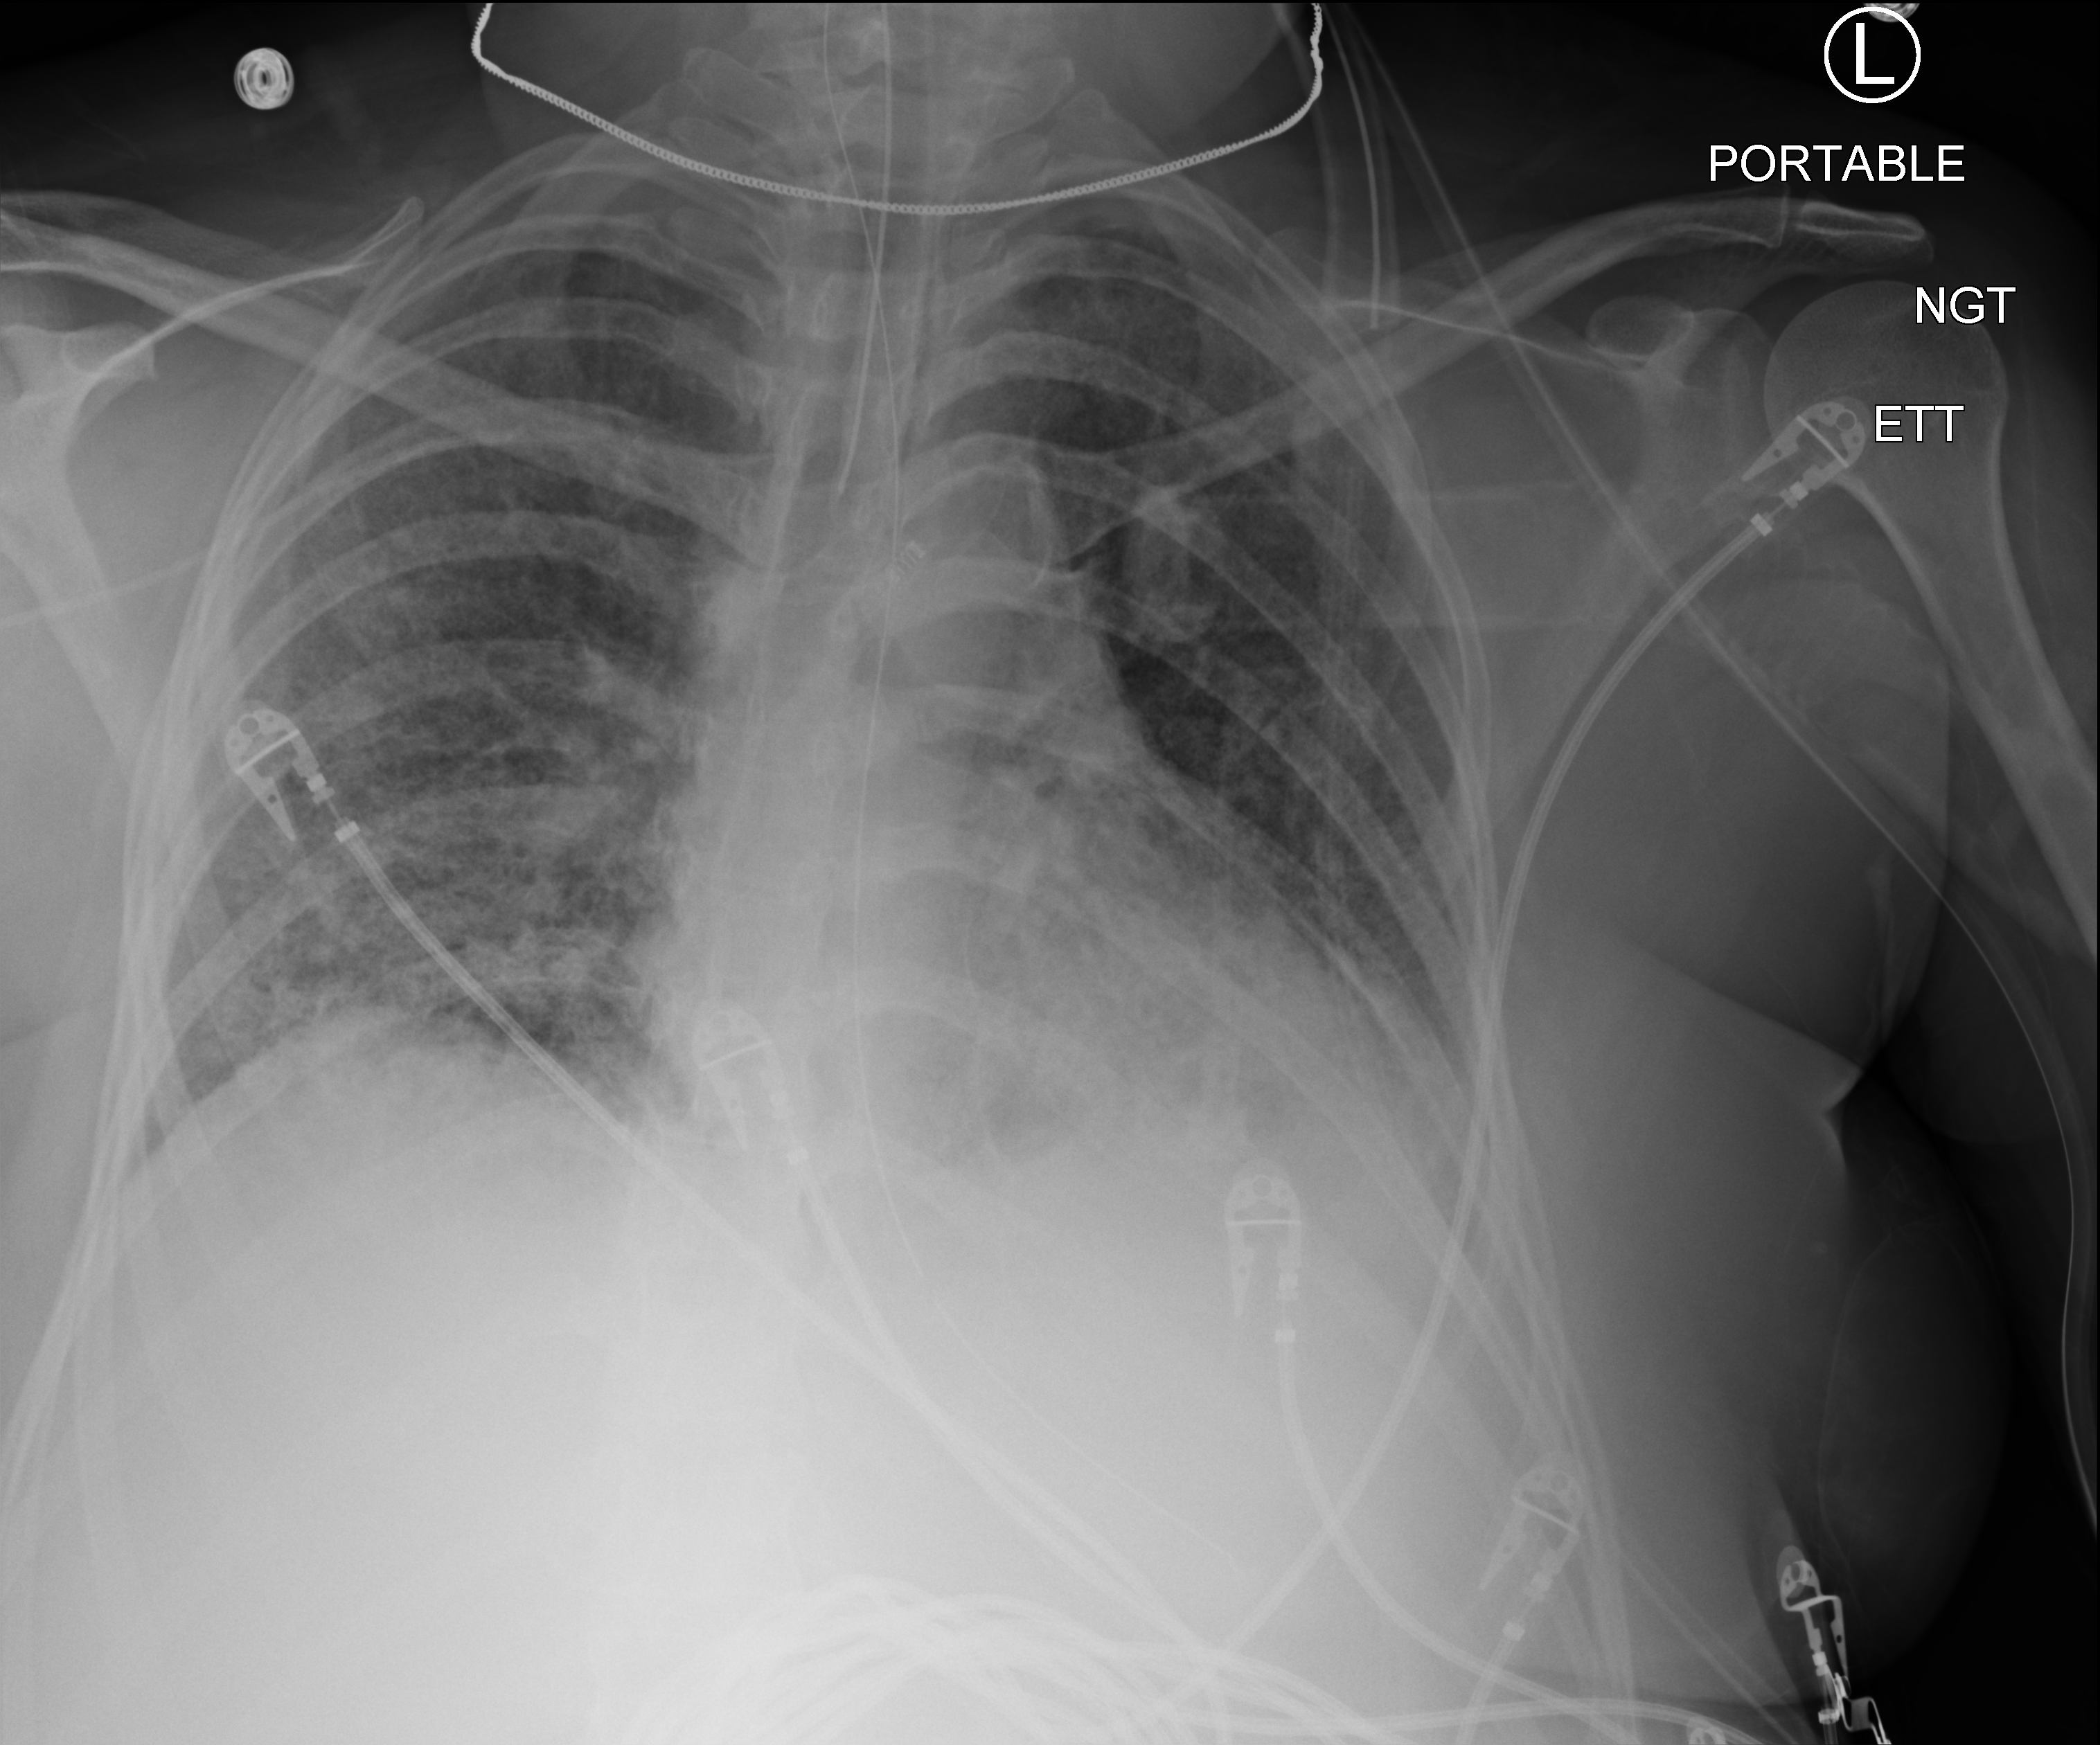
Bedside chest radiograph (computed radiography). Female patient hospitalised with COVID-19, age 18–59 years.
Admission-level facts for this patient (not findings on this image; timing relative to this image not recorded): mechanically ventilated during this hospital stay: yes; admitted to intensive care during this hospital stay: yes.